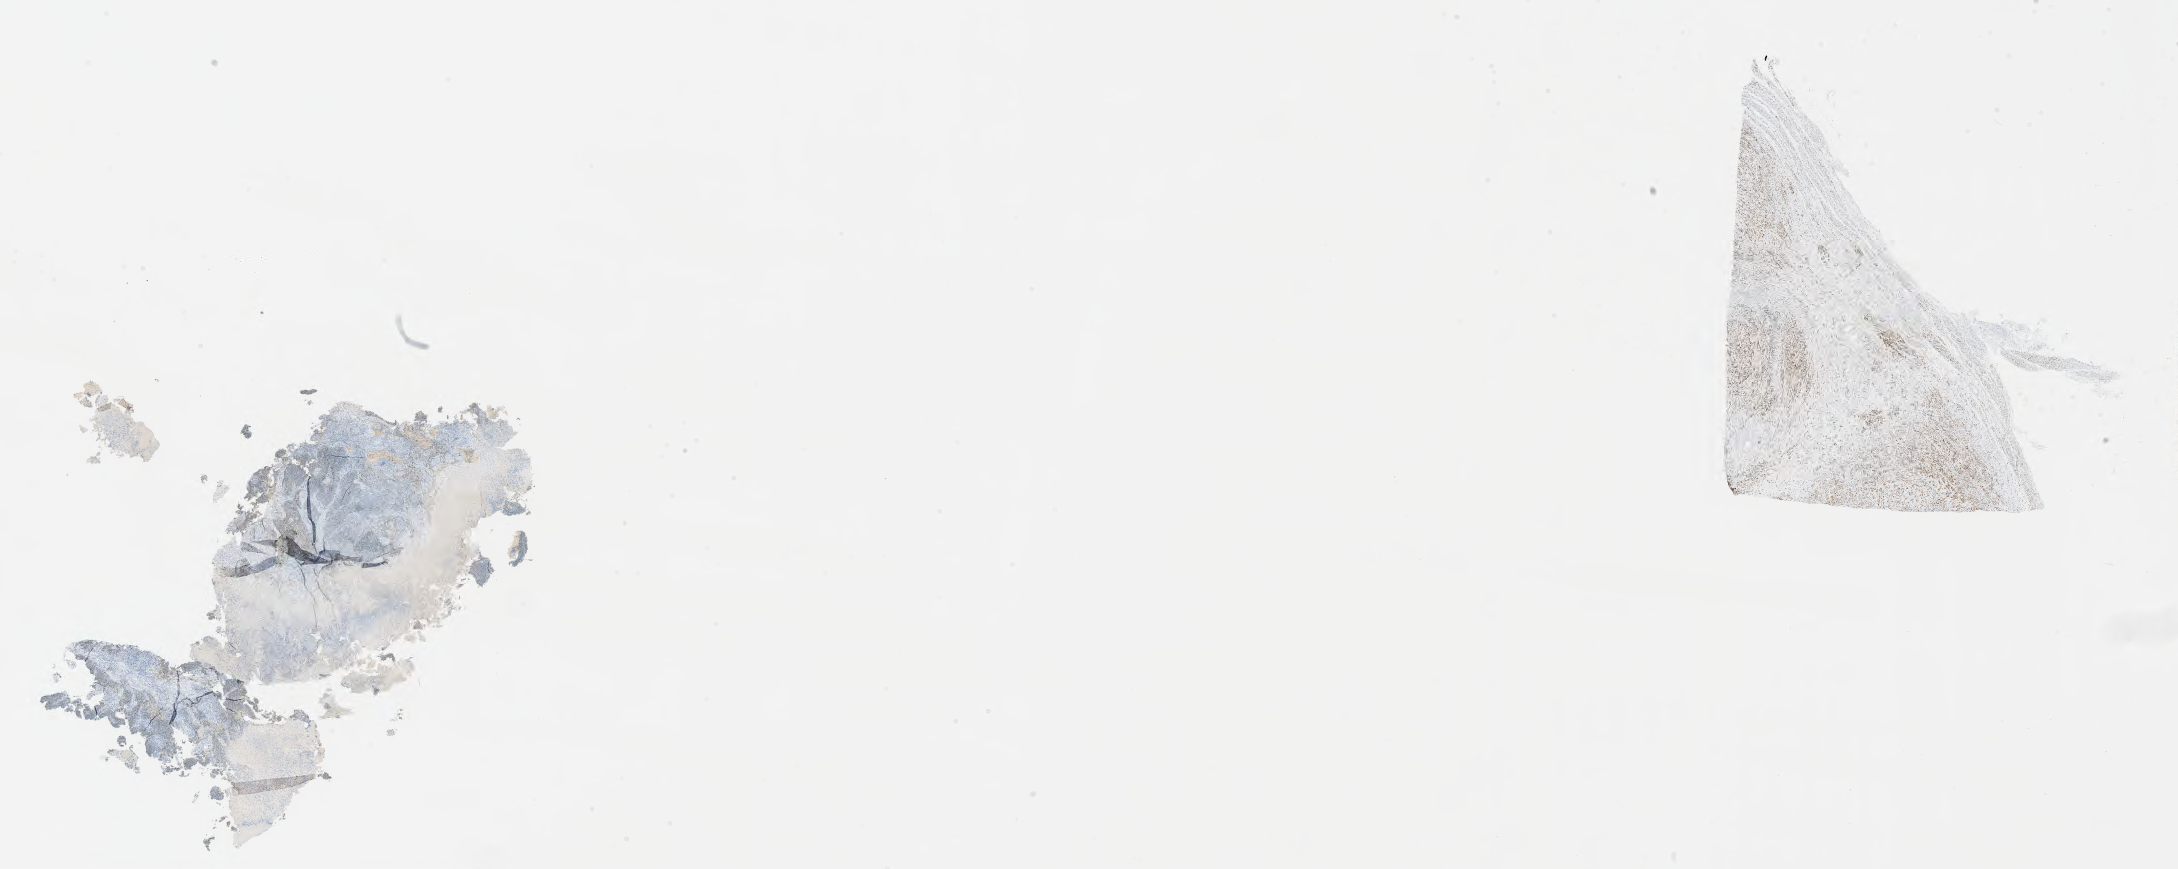
Immunohistochemistry (IHC) whole-slide image stained for progesterone receptor (PR), shown as a low-resolution overview of the whole scanned area (about 35.2 x 14.0 mm), tumor tissue, anatomic site: cervix. Patient: female, age 65 years.
Histologic diagnosis: Squamous cell carcinoma, large cell, nonkeratinizing, NOS.